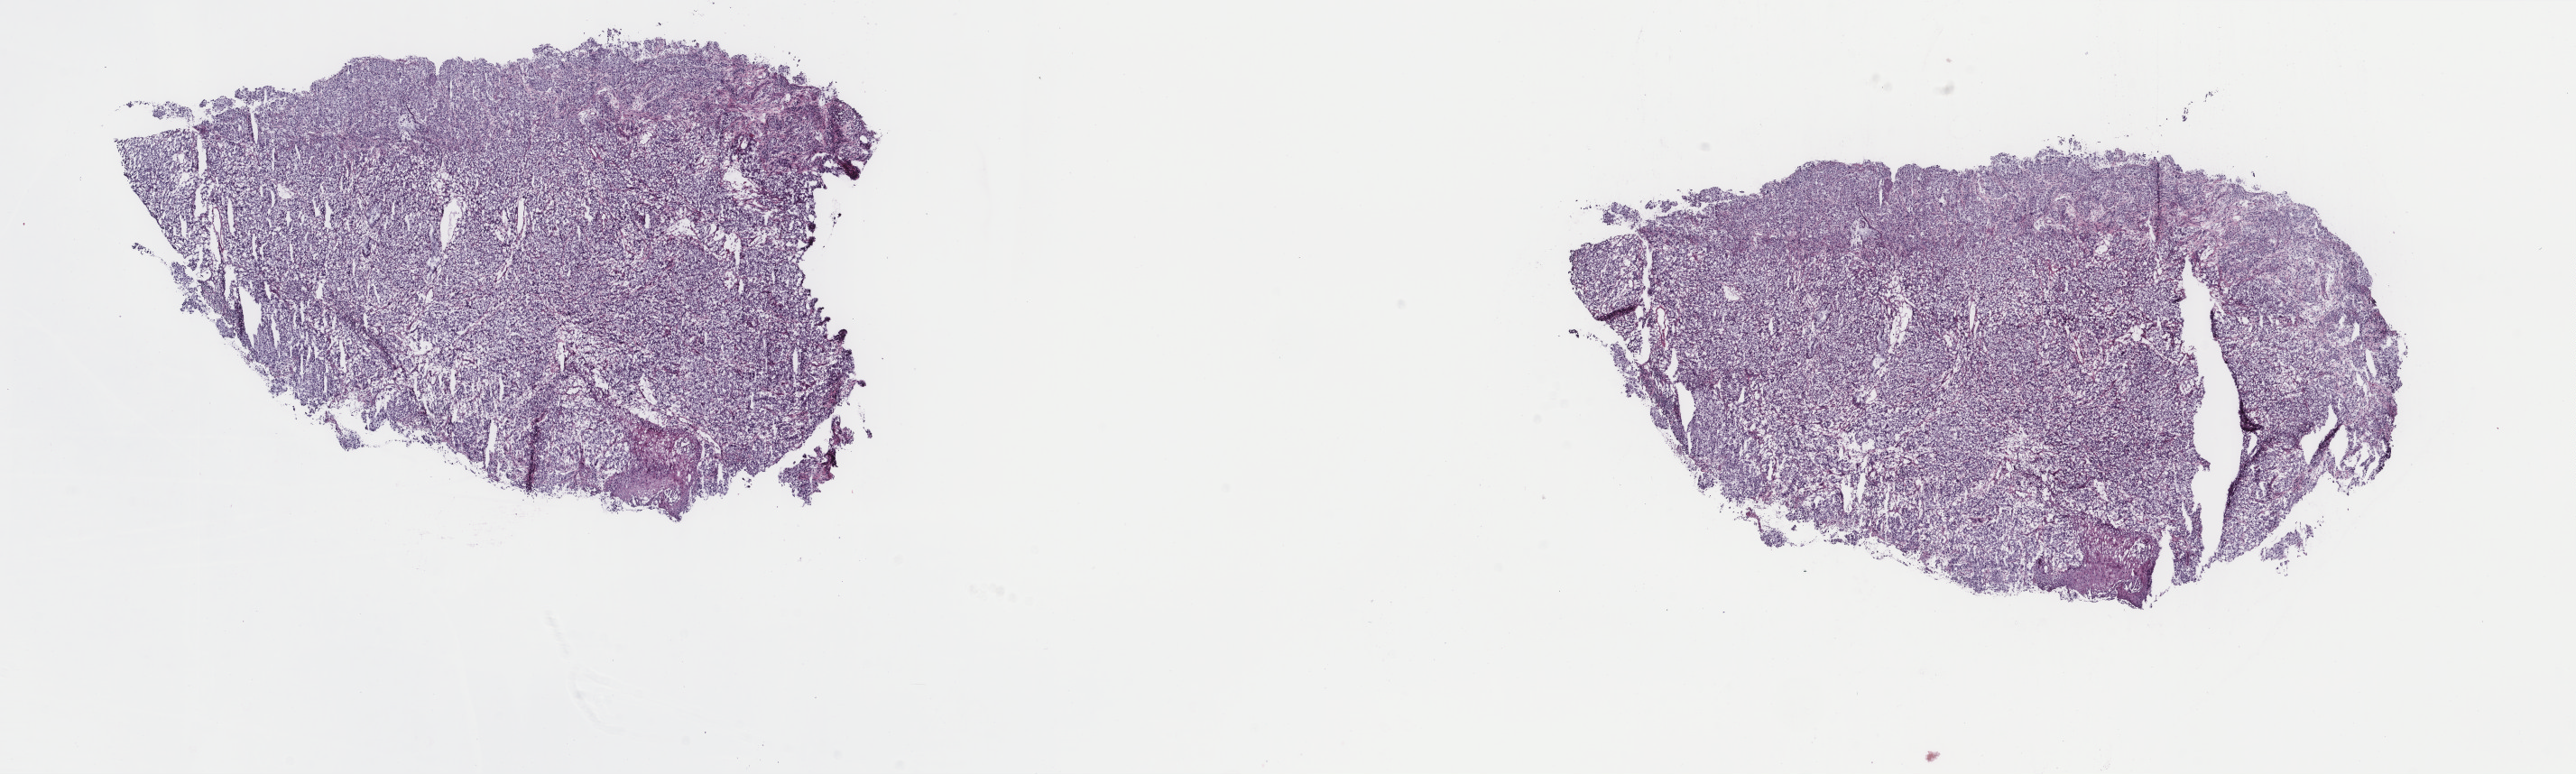
Digitized H&E-stained tissue section (whole slide), whole scanned area (about 22.7 x 6.8 mm, slide scanned at 40x) shown as a low-resolution overview. Frozen section from the top of the tissue portion. Primary tumour sample from the cervix. Female, age 35 years at initial diagnosis. Histologic grade: G3 (poorly differentiated). Pathologist review of this section (percent, as recorded): tumour cells 95%, tumour nuclei 80%, normal cells 3%, stromal cells 0%, necrosis 2%. Inflammatory infiltration, as recorded: lymphocyte infiltration 2%, monocyte infiltration 0%, neutrophil infiltration 0%.
Histologic diagnosis: Squamous cell carcinoma, NOS. FIGO stage: IIIB.